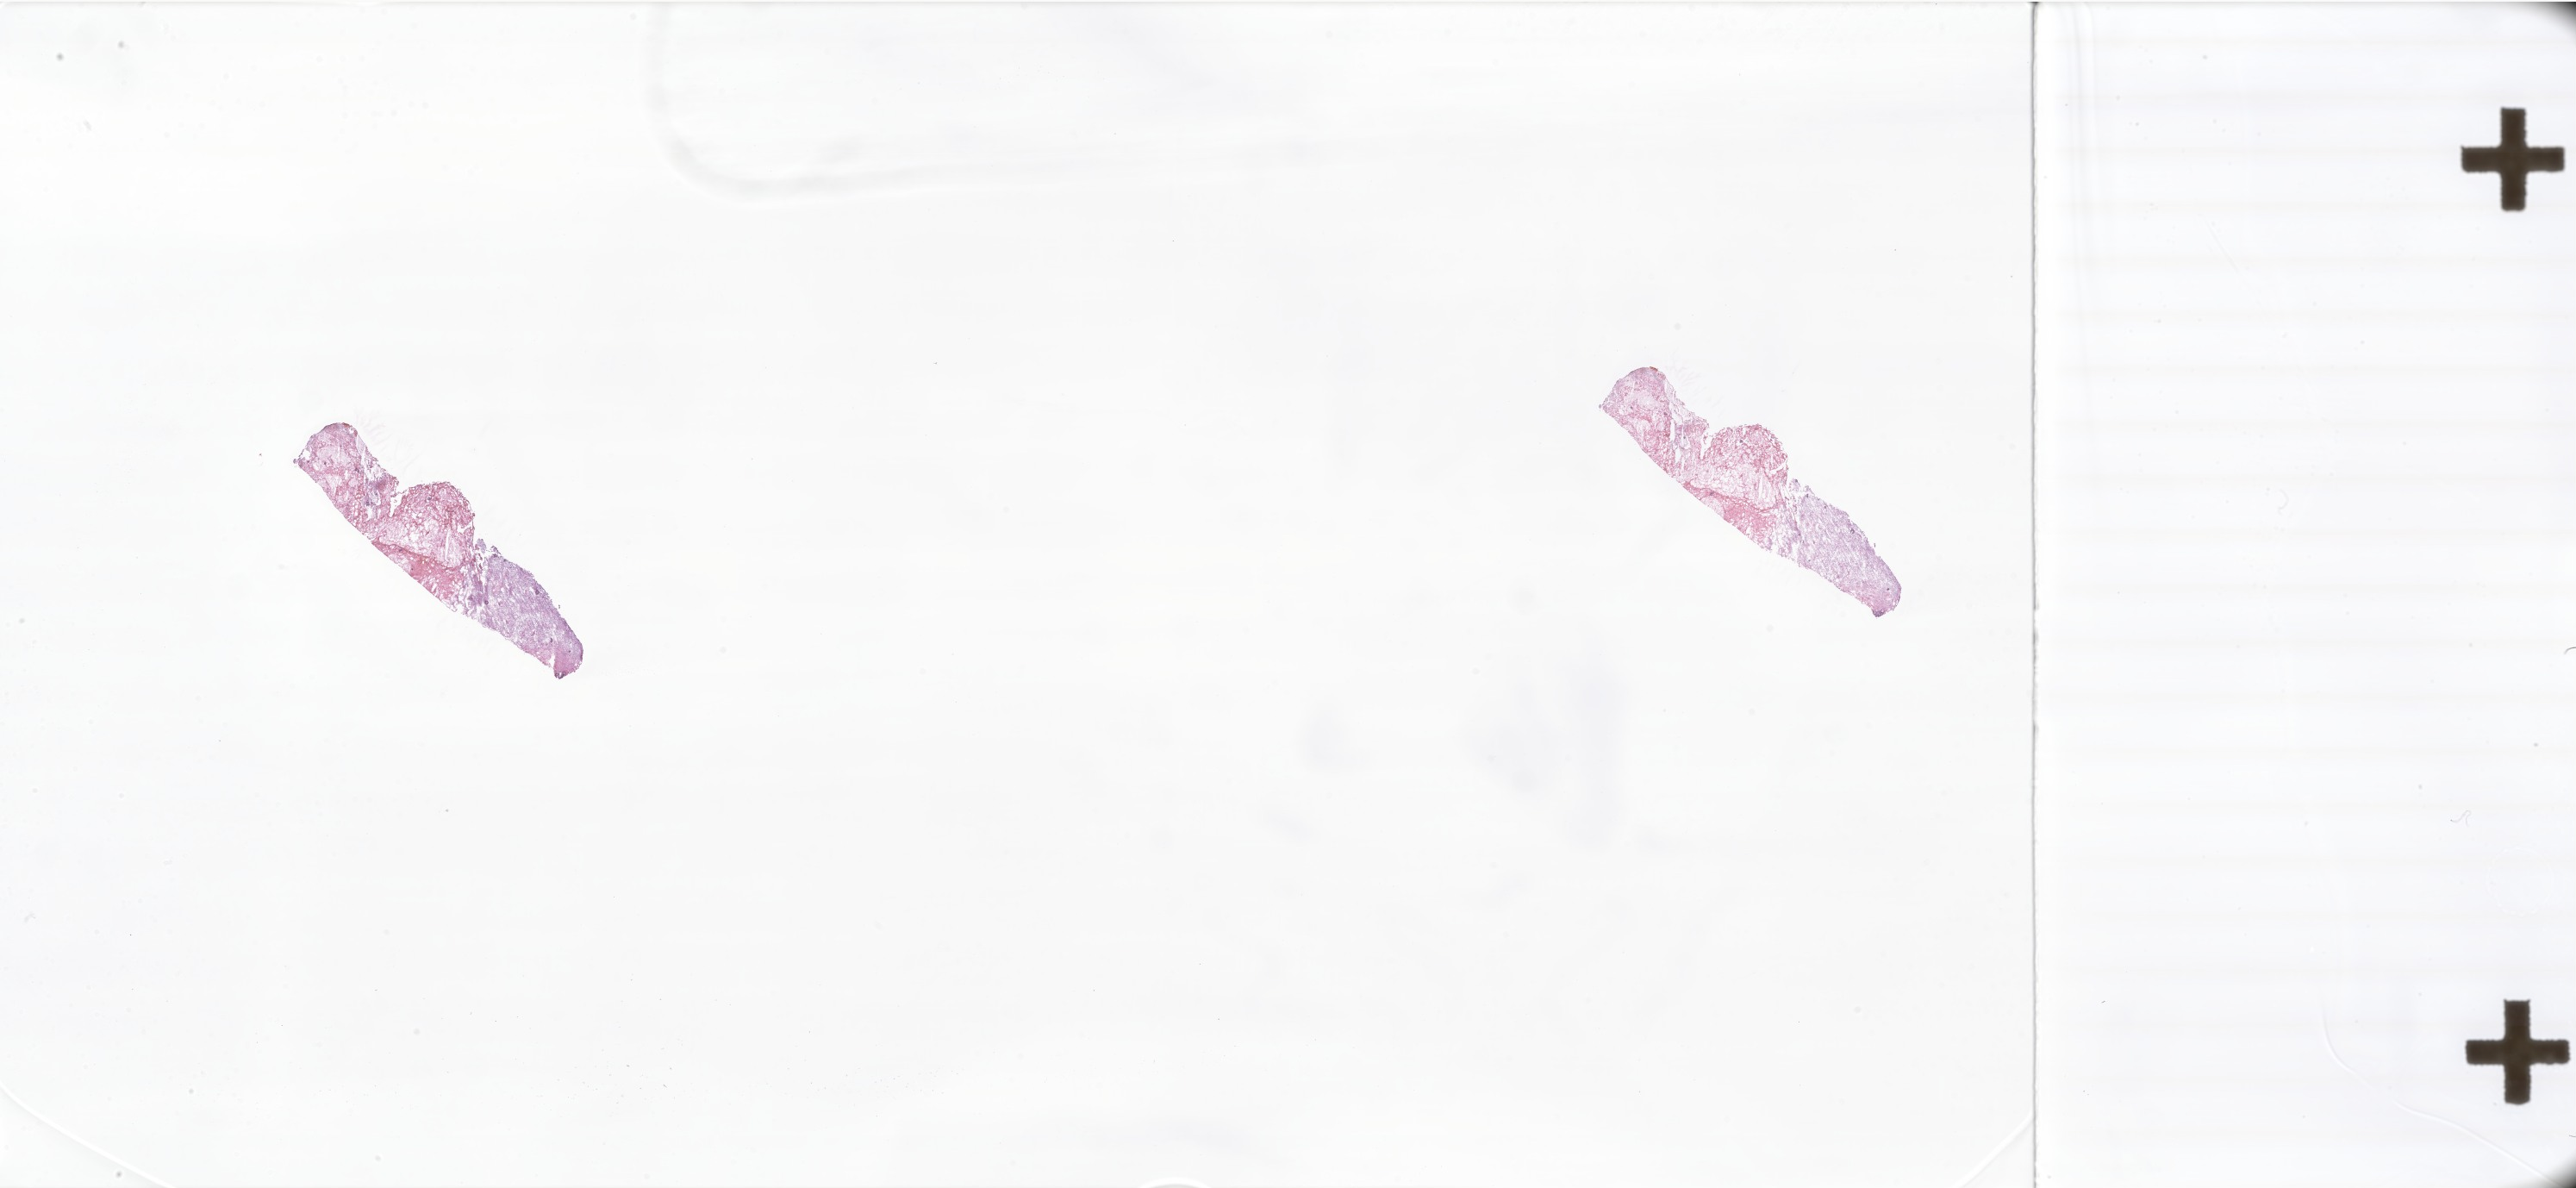
Whole-slide image, haematoxylin and eosin stain of tumor tissue from the brain — whole scanned area (about 50.4 x 23.2 mm) shown as a low-resolution overview; frozen section (OCT-embedded). Patient: female, age 219 months (18 years 3 months).
Diagnosis (ICD-O-3 morphology term): Pilocytic astrocytoma.